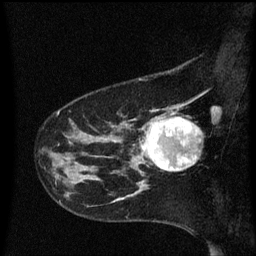
Breast MRI (dynamic contrast-enhanced), one sagittal slice; position 15 of 60 along the scan axis; dynamic contrast-enhanced series, image 2 of 3 at this slice position (ordered by acquisition); 1.5 T; TE 4.2 ms, TR 8.4 ms; 2 mm slice thickness; 256 × 256 image matrix, field of view 200 × 200 mm. Female patient, age 41 years. Case-level facts recorded for this patient, not image findings: setting: breast cancer imaged before/during neoadjuvant chemotherapy; receptor status: triple-negative.
Annotated regions visible in this slice (semi-automatically segmented with operator editing):
- analysis volume of interest (the breast-tissue region the enhancement analysis was run in; not a lesion): bounding box (x1, y1, x2, y2) in pixels: (138, 112, 200, 177)
- tumour enhancement mask (voxels above the 70 % enhancement threshold inside the analysis volume of interest): (141, 118, 199, 171)